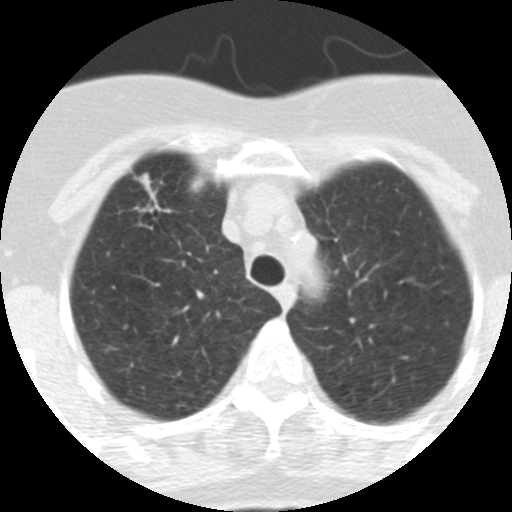
Low-dose screening chest CT, one axial slice; slice 251 of 313 in the series (ordered by position); reconstruction kernel STANDARD; 120 kVp; lung window (W 1500 / L -600 HU); 2.5 mm slice thickness; 512 × 512 image matrix.
Annotated regions visible in this slice (expert manual segmentation):
- lesion 1 (tumor, upper lobe of right lung): bounding box (x1, y1, x2, y2) in pixels: (134, 173, 159, 208)